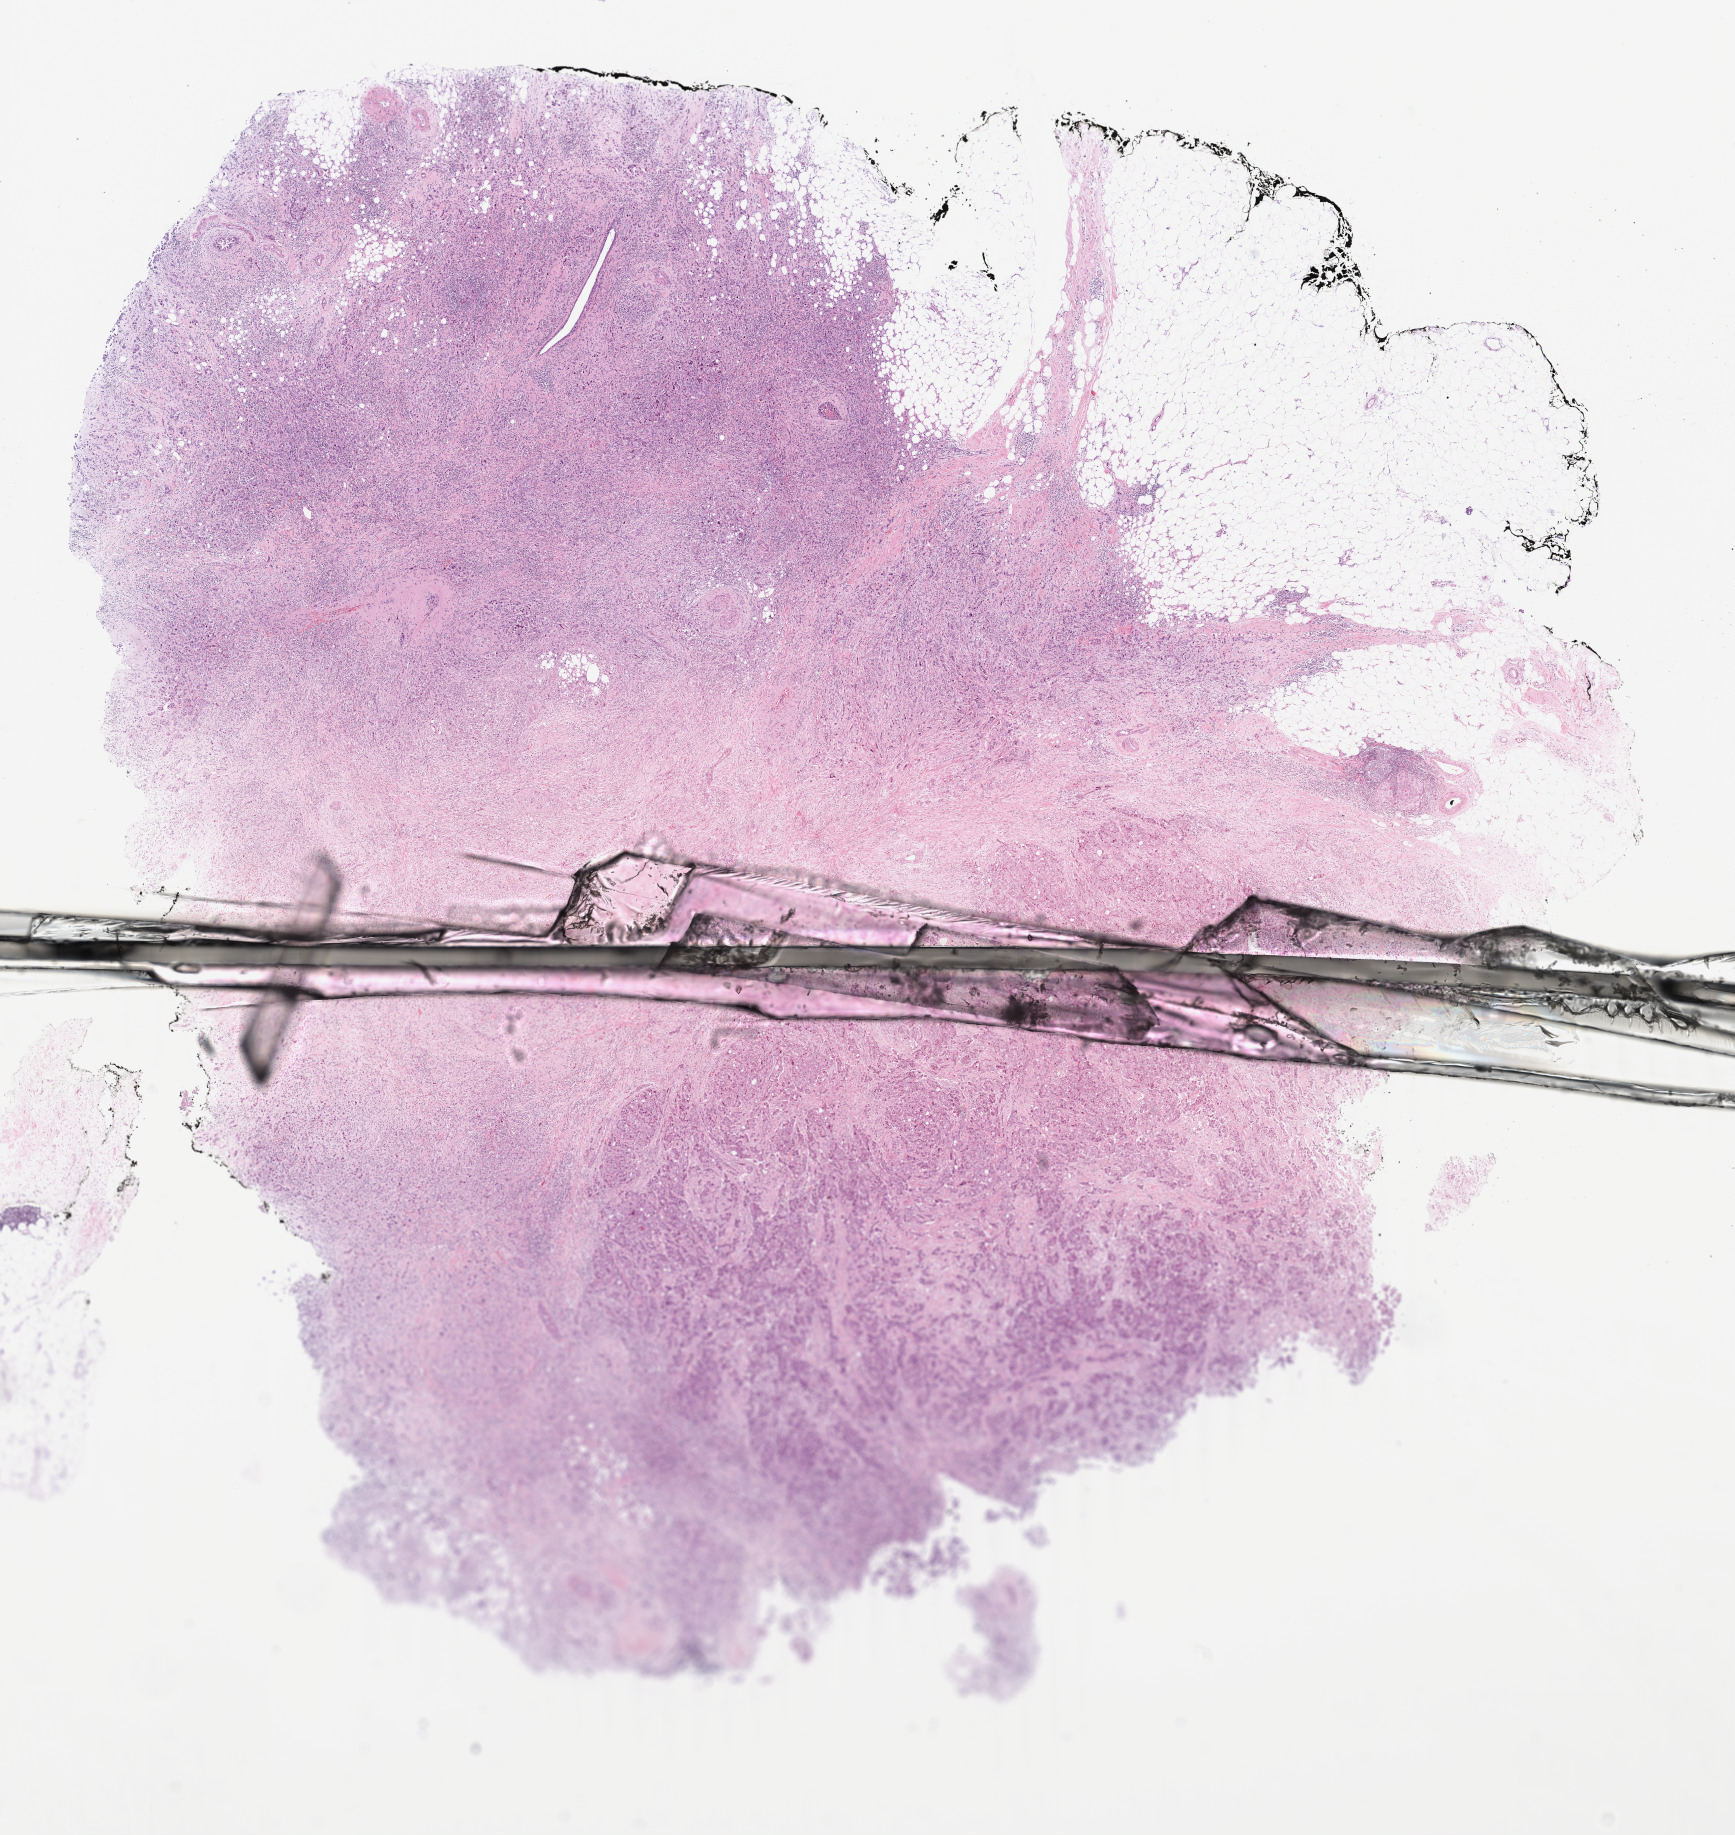
Digitized Hematoxylin and eosin (H&E) stained tissue section (whole slide) — low-resolution overview of the scanned area, about 13.8 x 14.6 mm; FFPE section; sample: primary tumour, thyroid. Female patient; age at initial diagnosis 47 years.
TNM: T2 N1a MX. Laterality: left. Histologic diagnosis: Papillary adenocarcinoma, NOS (thyroid gland). AJCC pathologic stage: III (7th edition).